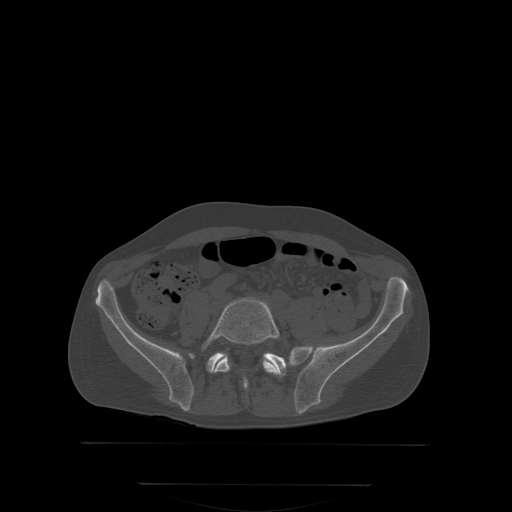
CT including the spine, one axial slice; position 92 of 350 along the scan axis; bone window (W 1800 / L 400 HU); 512 × 512 image matrix, field of view 500 × 500 mm. Male patient, age 58 years. From the clinical record (not read from this slice): primary cancer: prostate.
Structures marked on this image (semi-automatically segmented with operator editing):
- L5 vertebra: bounding box [x1, y1, x2, y2] px = [206, 298, 281, 389]